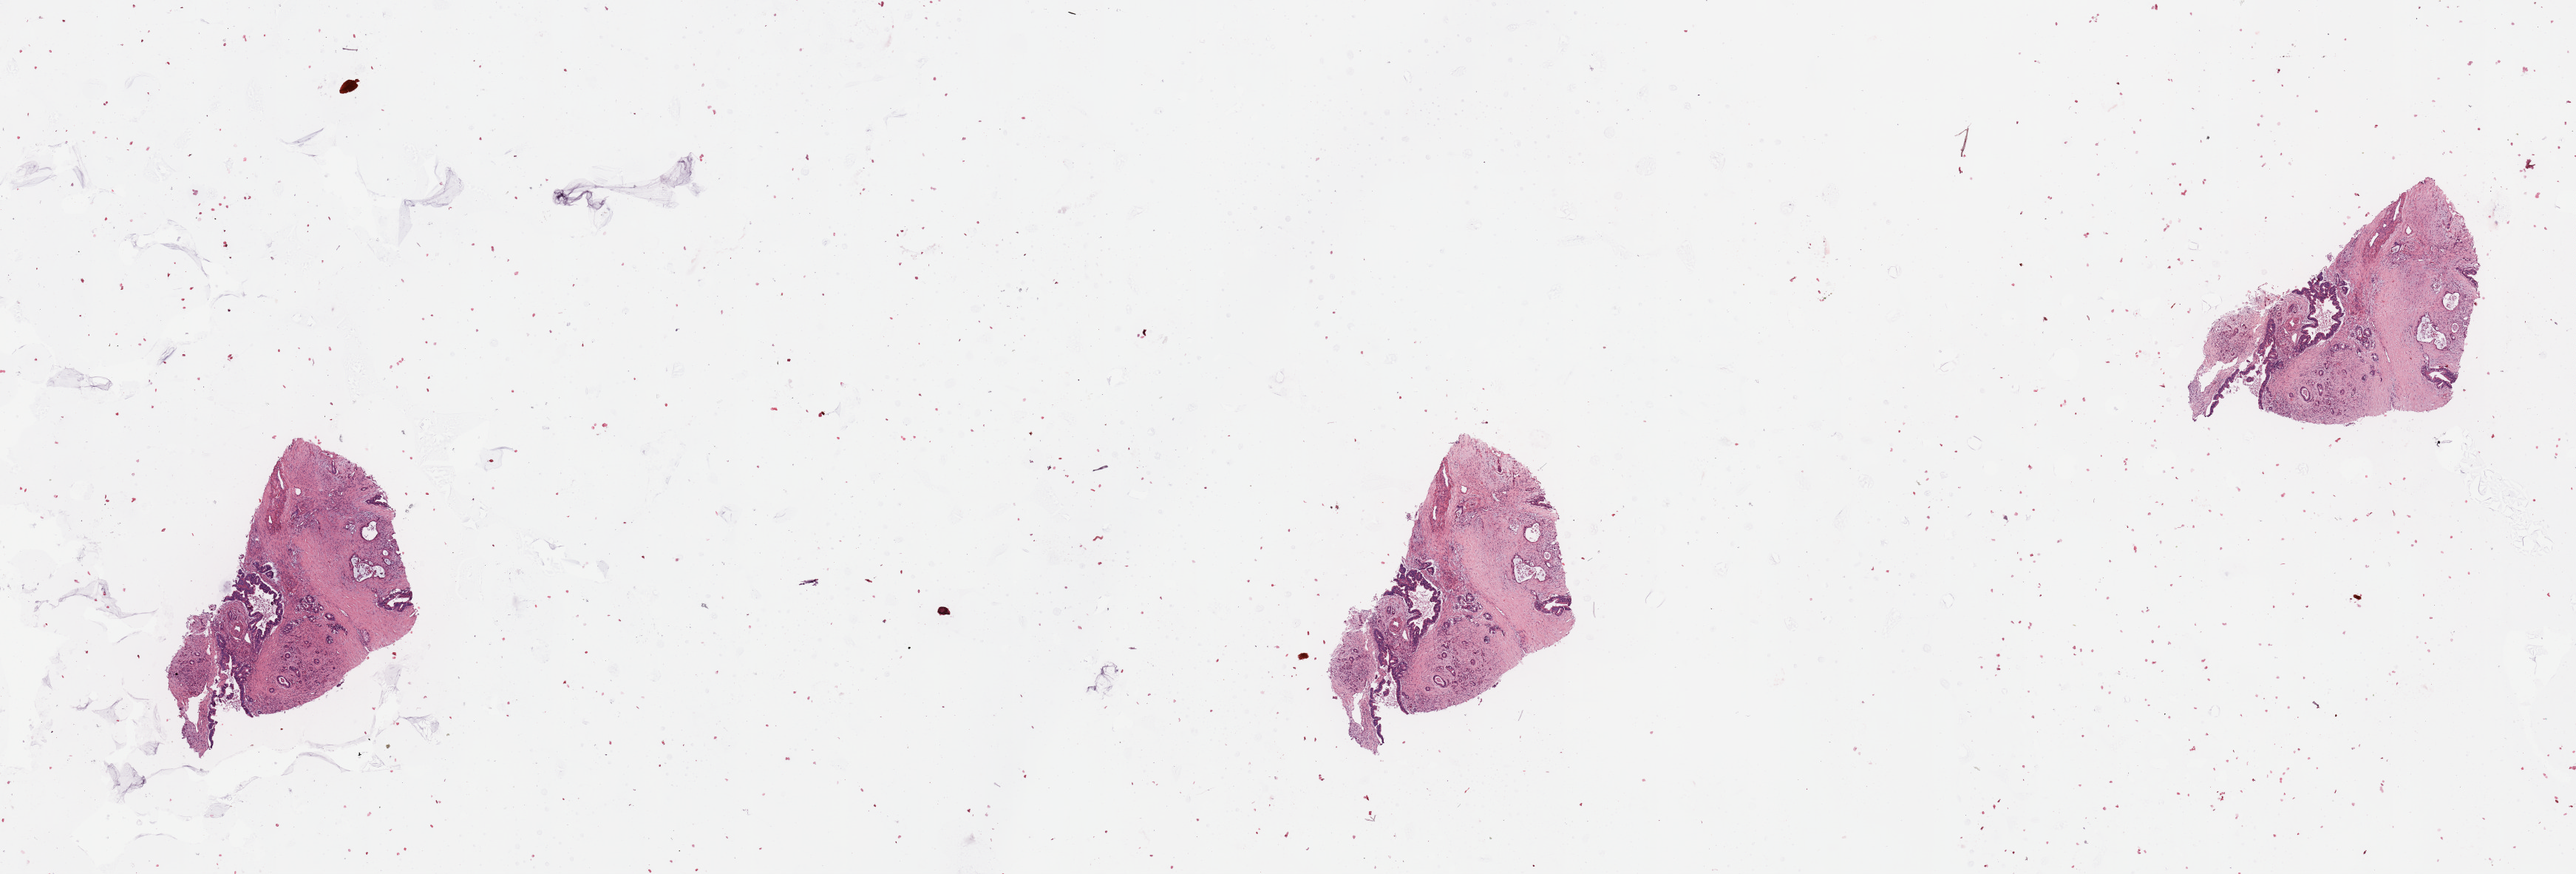
H&E whole-slide image, low-resolution overview of the scanned area, about 27.6 x 9.3 mm (from a 20x scan); tumour tissue sample, sampled site: pancreas. 77-year-old female patient. Histologic grade: G2 (moderately differentiated). Pathologist review of this section (percent, as recorded): tumour nuclei 25%, necrosis 2%.
Primary tumour site (as recorded): head. Histologic diagnosis: Infiltrating duct carcinoma, NOS. AJCC pathologic stage: IIB.